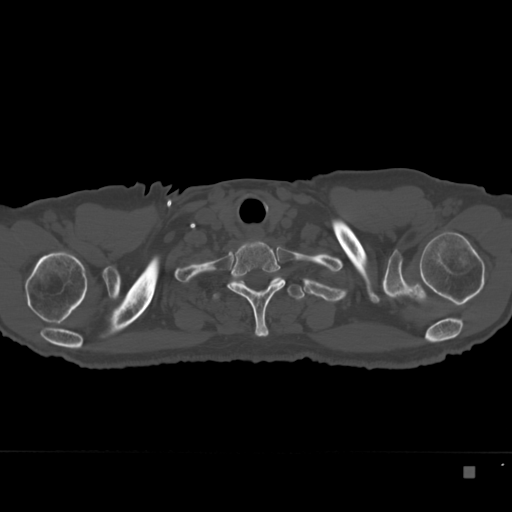
CT including the spine, one axial slice. Position 313 of 332 along the scan axis. 120 kVp. Bone window (W 1800 / L 400 HU). 512 × 512 image matrix, field of view 389 × 389 mm. Patient: male, 72 years. From the clinical record (not read from this slice): primary cancer: skeletal.
Outlined on this slice (semi-automatically segmented with operator editing):
- T1 vertebra: bounding box (x1, y1, x2, y2) in pixels: (227, 240, 285, 337)
- T2 vertebra: (213, 276, 306, 300)